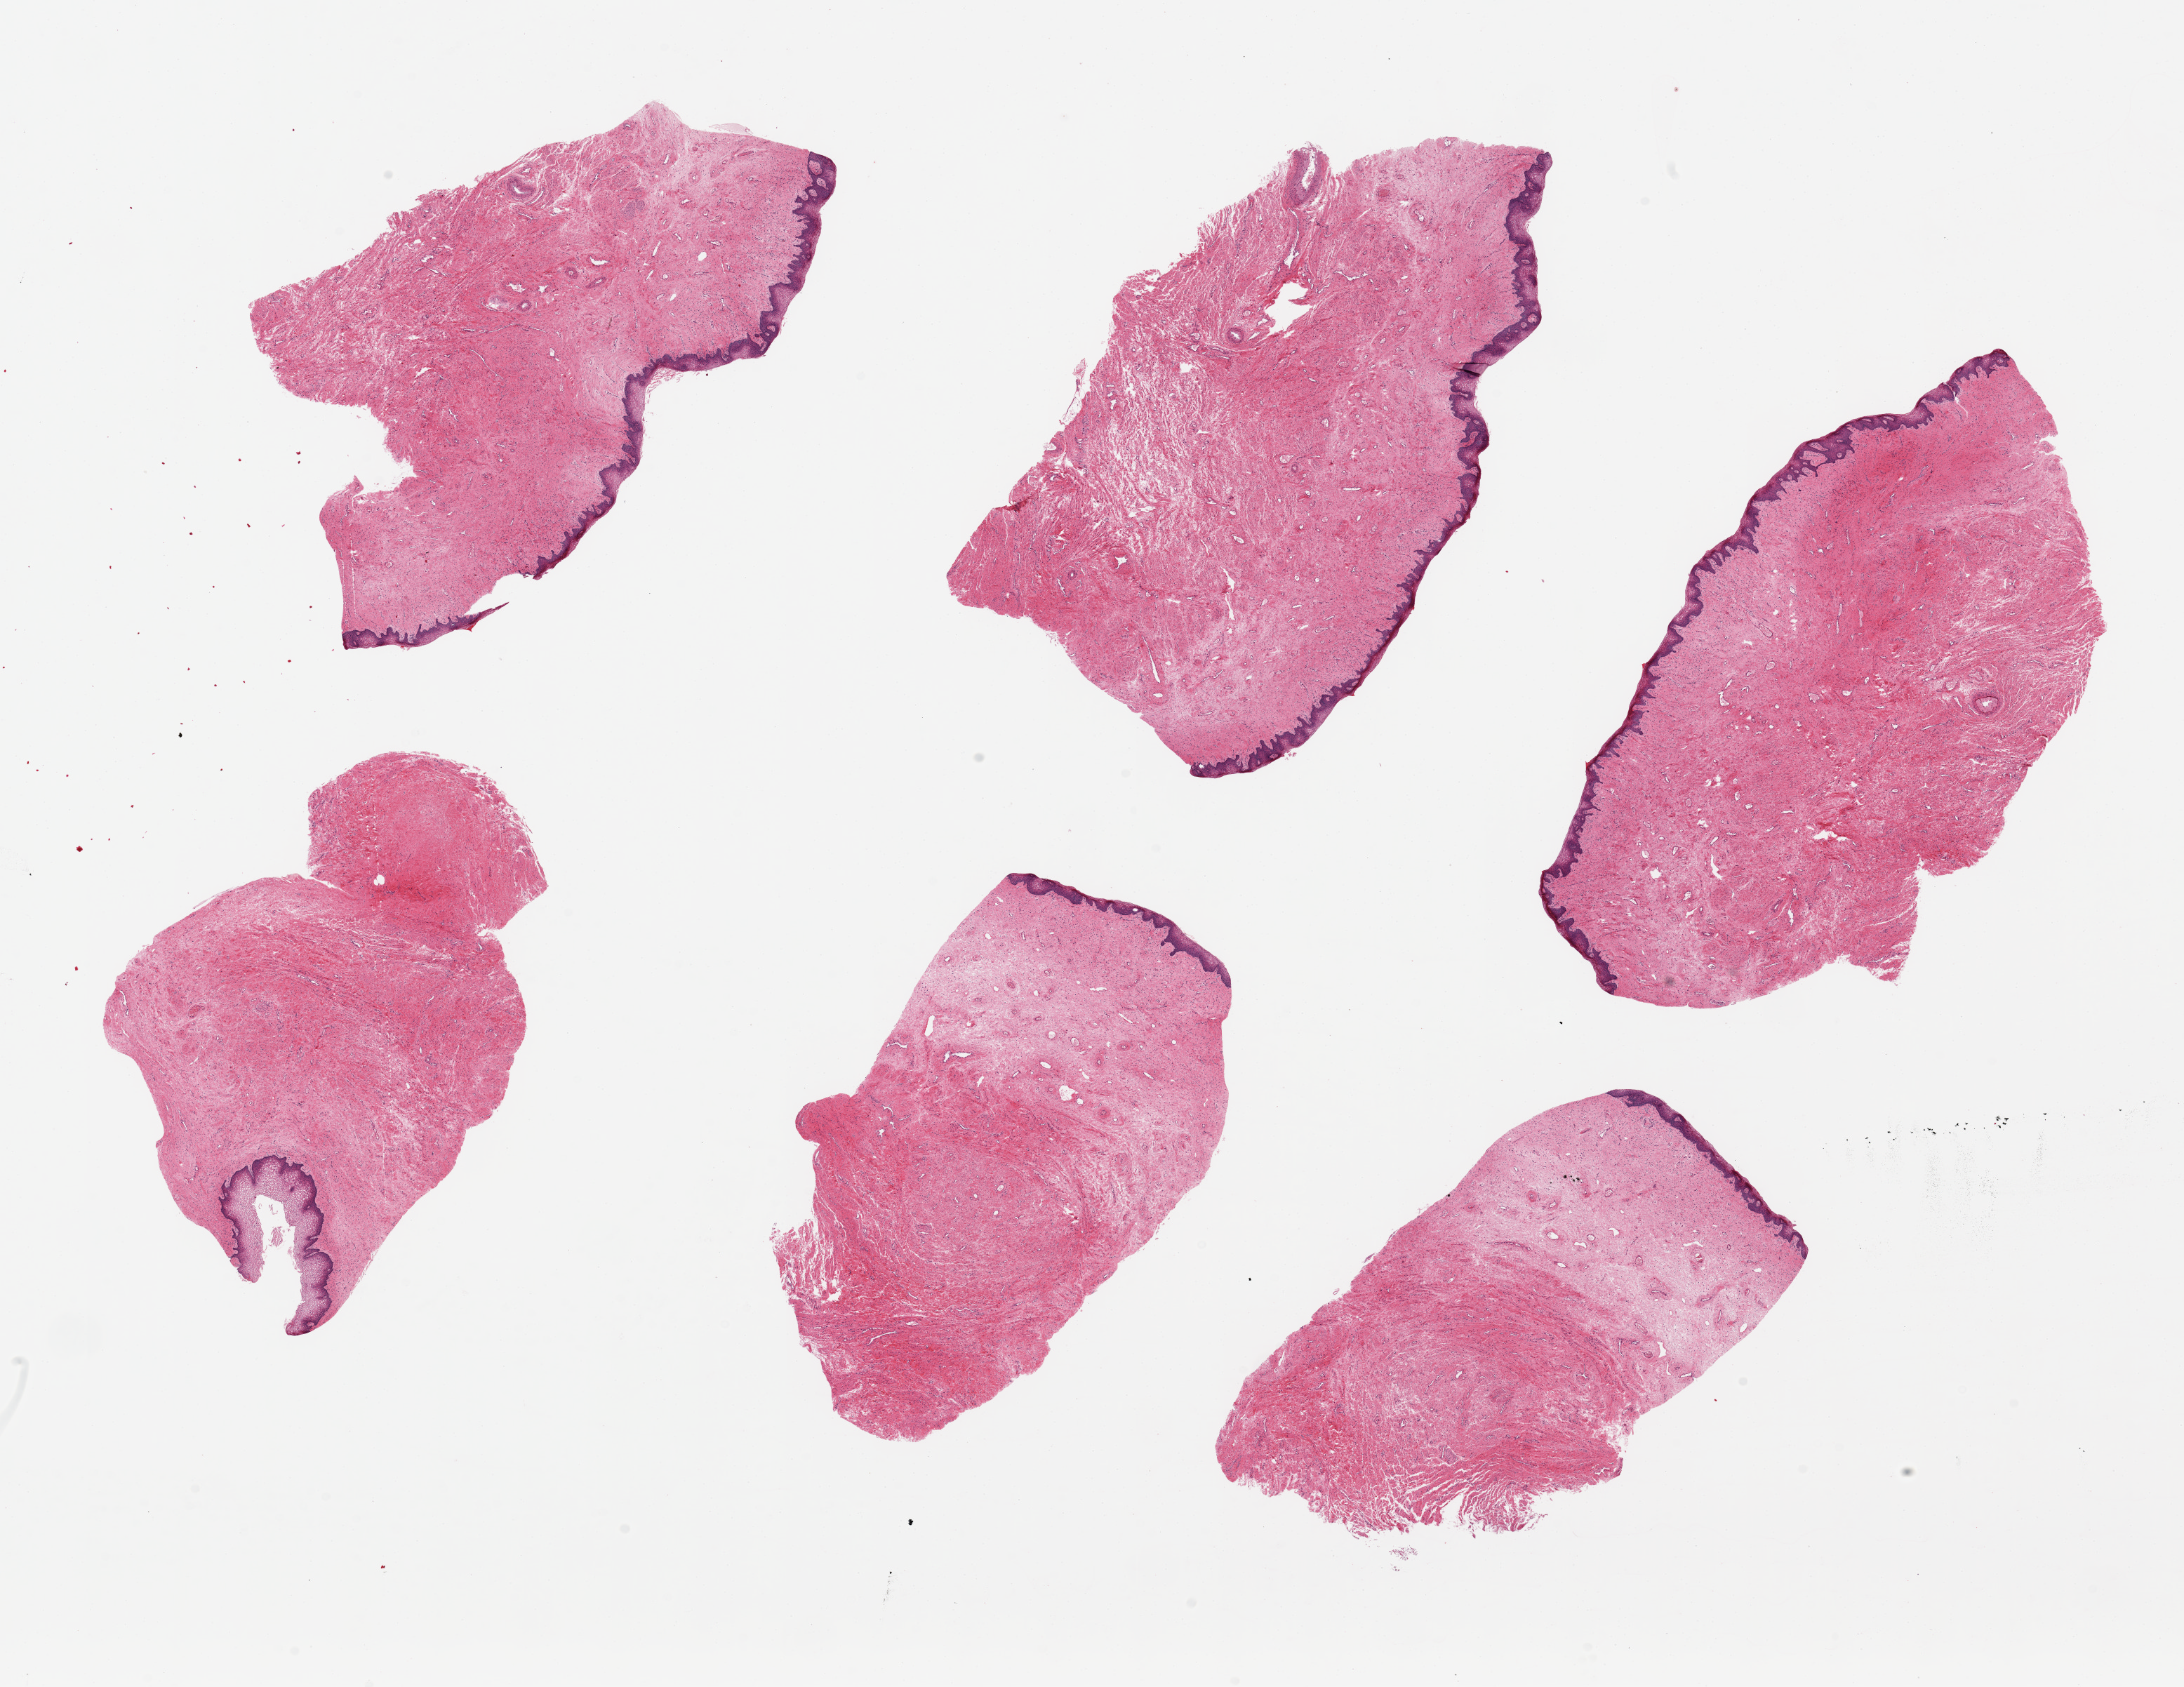
Whole-slide image, hematoxylin and eosin (H&E) stain, brightfield, shown as a low-resolution overview of the whole scanned area (about 24.6 x 19.0 mm, acquisition: 20x scan), PAXgene-fixed, paraffin-embedded tissue, sampled site (target tissue): vagina, tissue donor sample. Female donor.
* reviewer comment on this tissue sample: 6 pieces up to 8x4 mm; all with epithelium